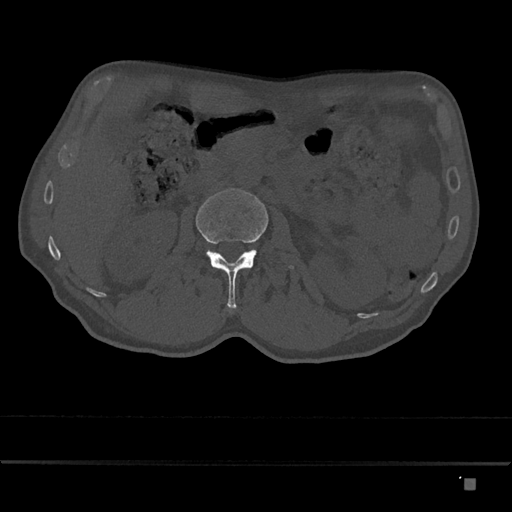
CT including the spine, one axial slice. Slice 471 of 797 in the series (ordered by position). Reconstruction kernel Br40s/3. 120 kVp. Bone window (W 1800 / L 400 HU). 512 × 512 image matrix, field of view 390 × 390 mm. Patient: male, 72 years. Case-level facts recorded for this patient, not image findings: primary cancer: prostate.
Outlined on this slice (semi-automatically segmented with operator editing):
- L2 vertebra: bounding box [x1, y1, x2, y2] px = [196, 188, 293, 309]